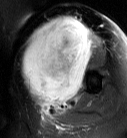
MRI of an extremity soft-tissue mass, one axial slice. Position 47 of 87 along the scan axis. T2-weighted fat-saturated. MR volume resampled by the dataset authors to the PET/CT grid (not the native acquisition matrix). 3.27 mm slice thickness. 127 × 138 image matrix, field of view 124 × 135 mm. Female patient. From the clinical record (not read from this slice): histological type: pleiomorphic leiomyosarcoma; grade: high; site of the primary tumour: left biceps.
Structures marked on this image (expert contour drawn on MRI and transferred to this co-registered scan by the dataset authors):
- gross tumour volume including surrounding oedema: bounding box [x1, y1, x2, y2] px = [20, 16, 99, 113]
- gross tumour volume (mass): [22, 16, 92, 106]